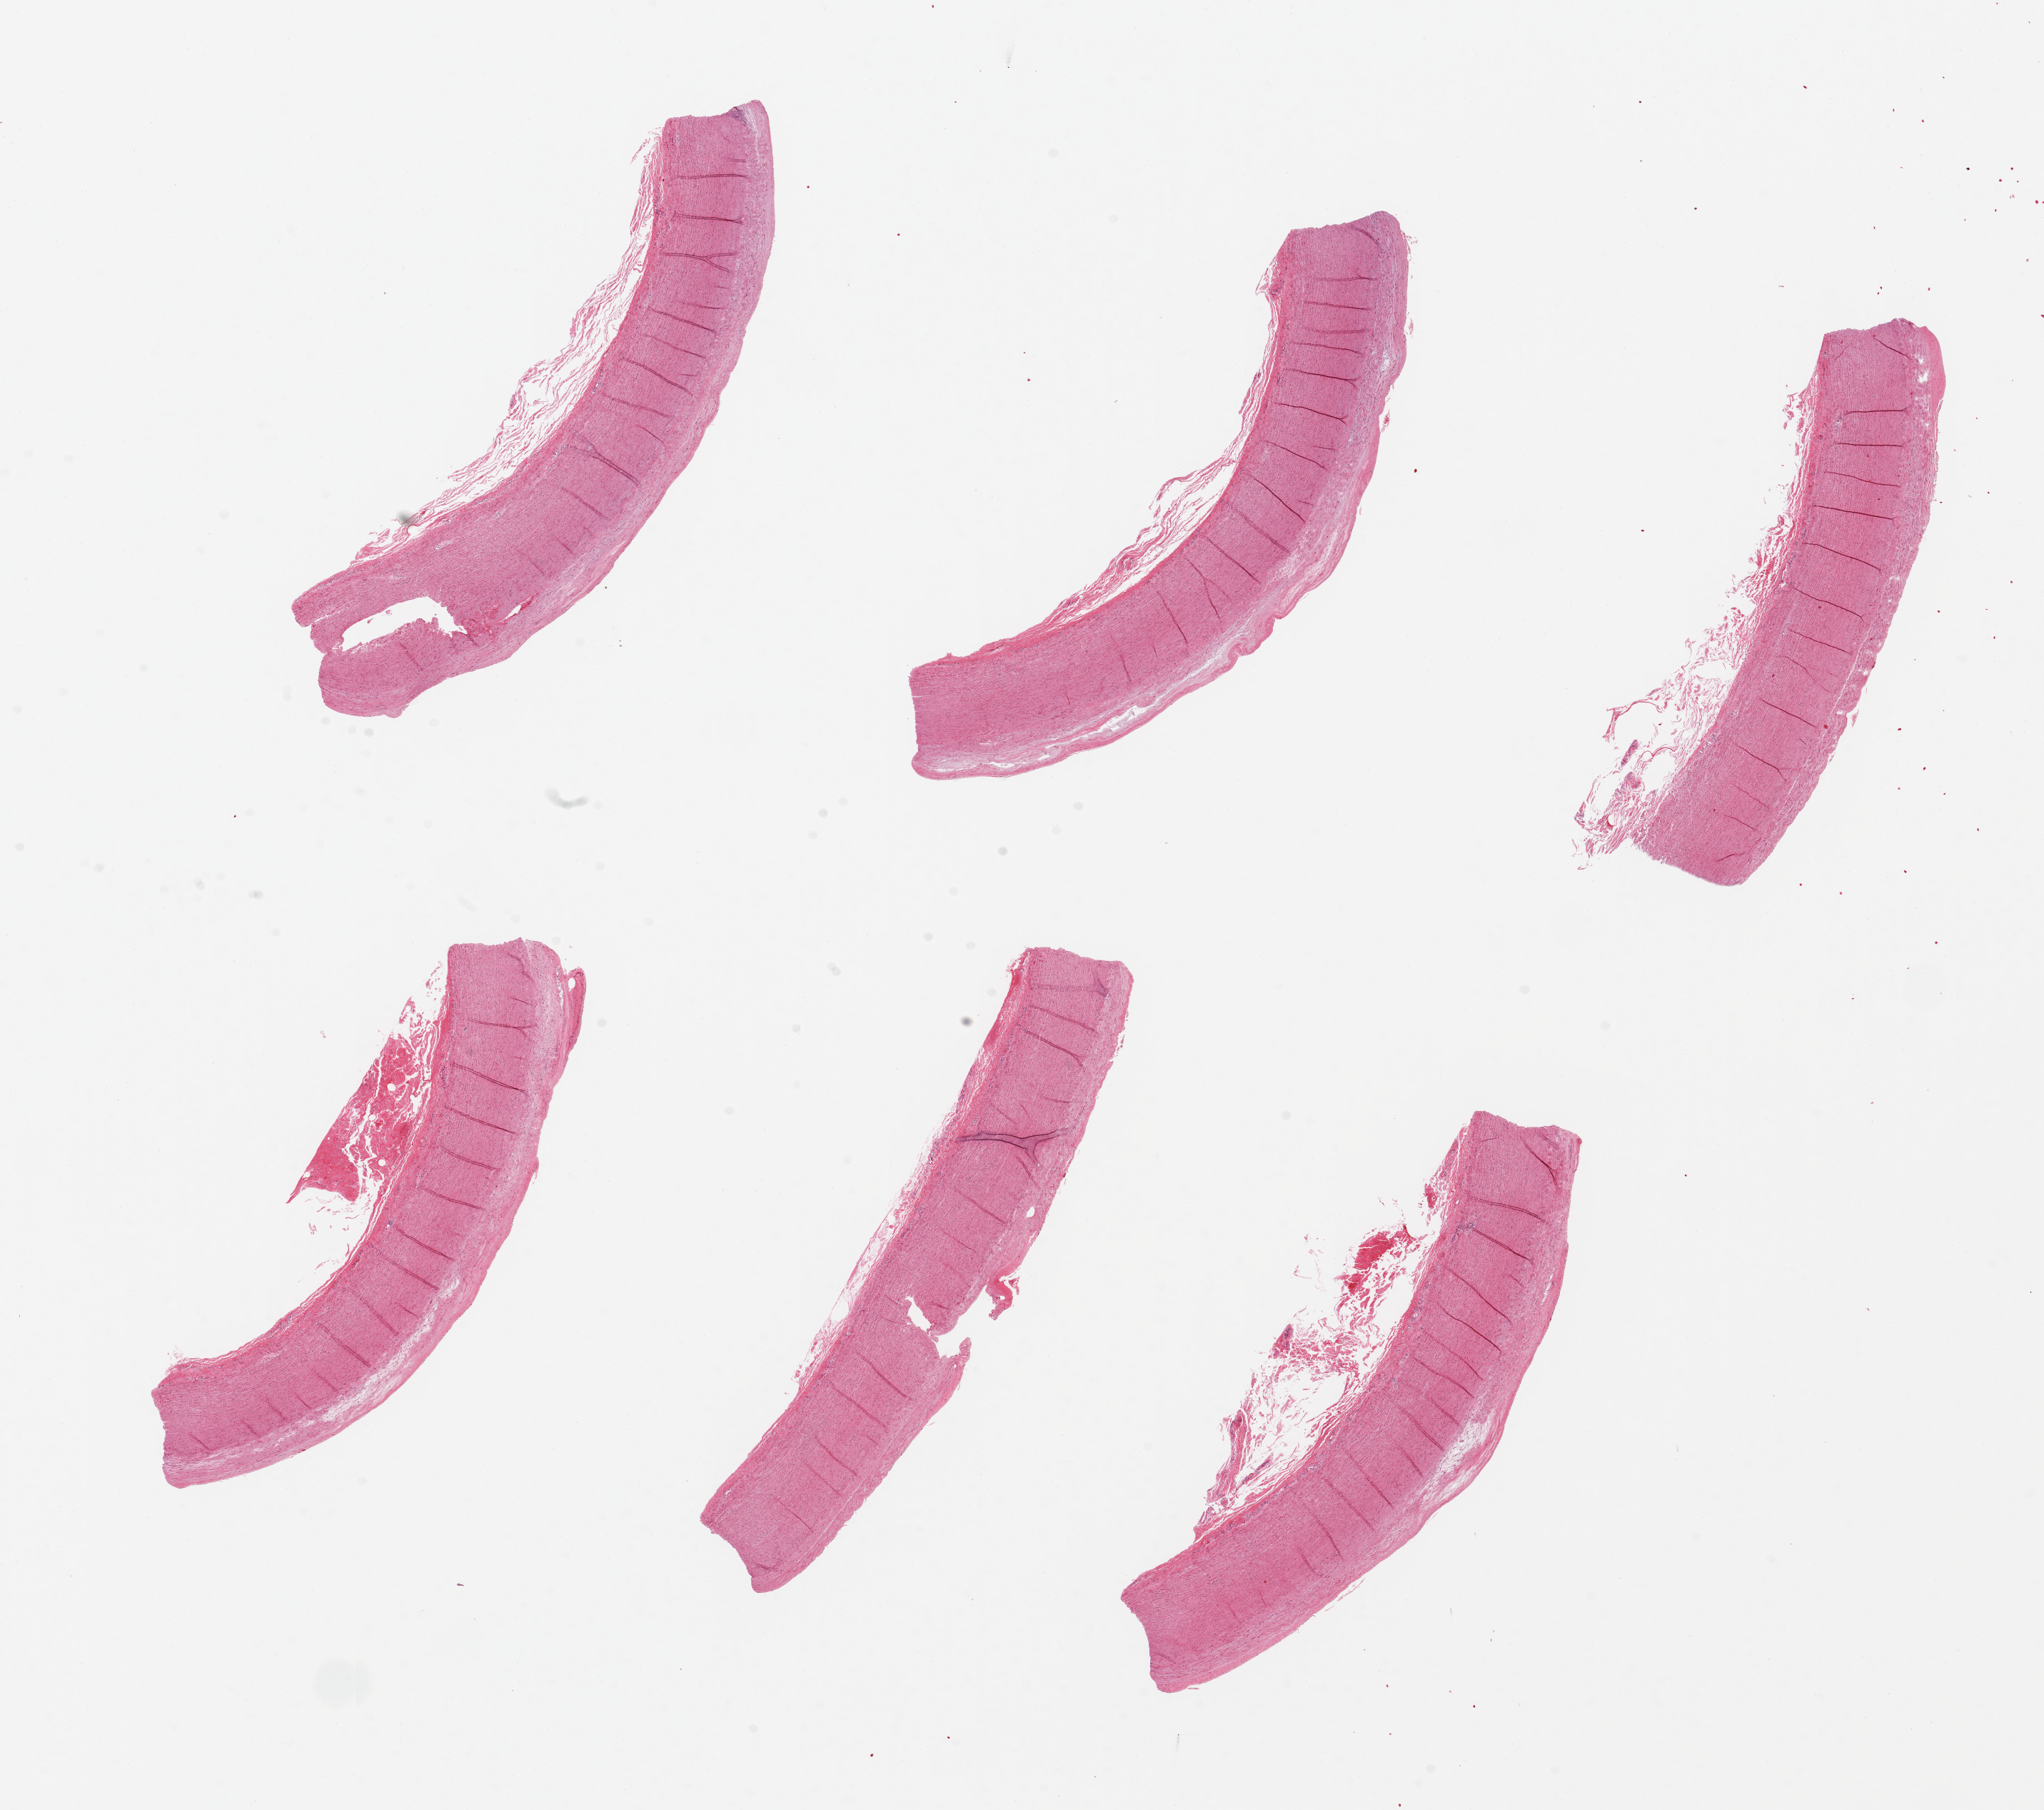
Digitized haematoxylin and eosin-stained section, brightfield, a low-resolution overview of the entire scanned area, about 22.6 x 20.0 mm. PAXgene-fixed, paraffin-embedded tissue. Sampled site (target tissue): aorta. Donor tissue sample. Donor sex: male.
Review note (as recorded): 6 pieces up to 1.5x8 mm; flat plaques up to 0.4mm.